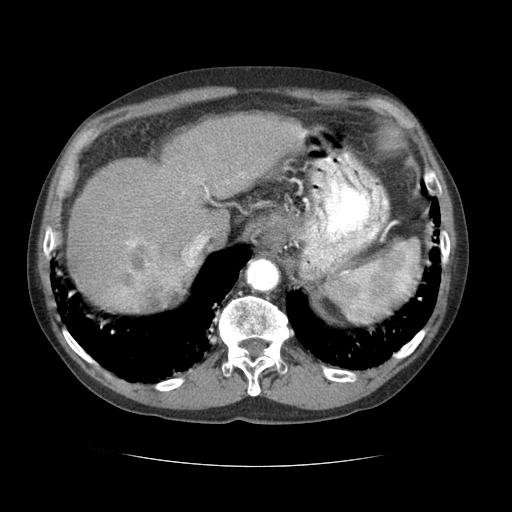
Contrast-enhanced abdominal CT (liver protocol), one axial slice. Slice 52 of 69 in the series (ordered by position). 120 kVp. Soft-tissue window (W 400 / L 40 HU). 2.5 mm slice thickness. 512 × 512 image matrix, field of view 360 × 360 mm. Case-level facts recorded for this patient, not image findings: diagnosis: hepatocellular carcinoma (patient treated with transarterial chemoembolisation; whether this scan precedes or follows treatment is not stated here); TNM stage (as recorded): Stage-II; Child-Pugh class: B; tumour differentiation: poorly differentiated; tumour size: 2.6 cm.
Annotated regions visible in this slice (semi-automatically segmented with operator editing):
- liver parenchyma outside the tumour (the mass and vessels are separate outlines, so this box may not span the whole liver): bounding box (x1, y1, x2, y2) in pixels: (66, 114, 307, 310)
- mass: (101, 235, 188, 312)
- liver vessels: (126, 132, 305, 268)